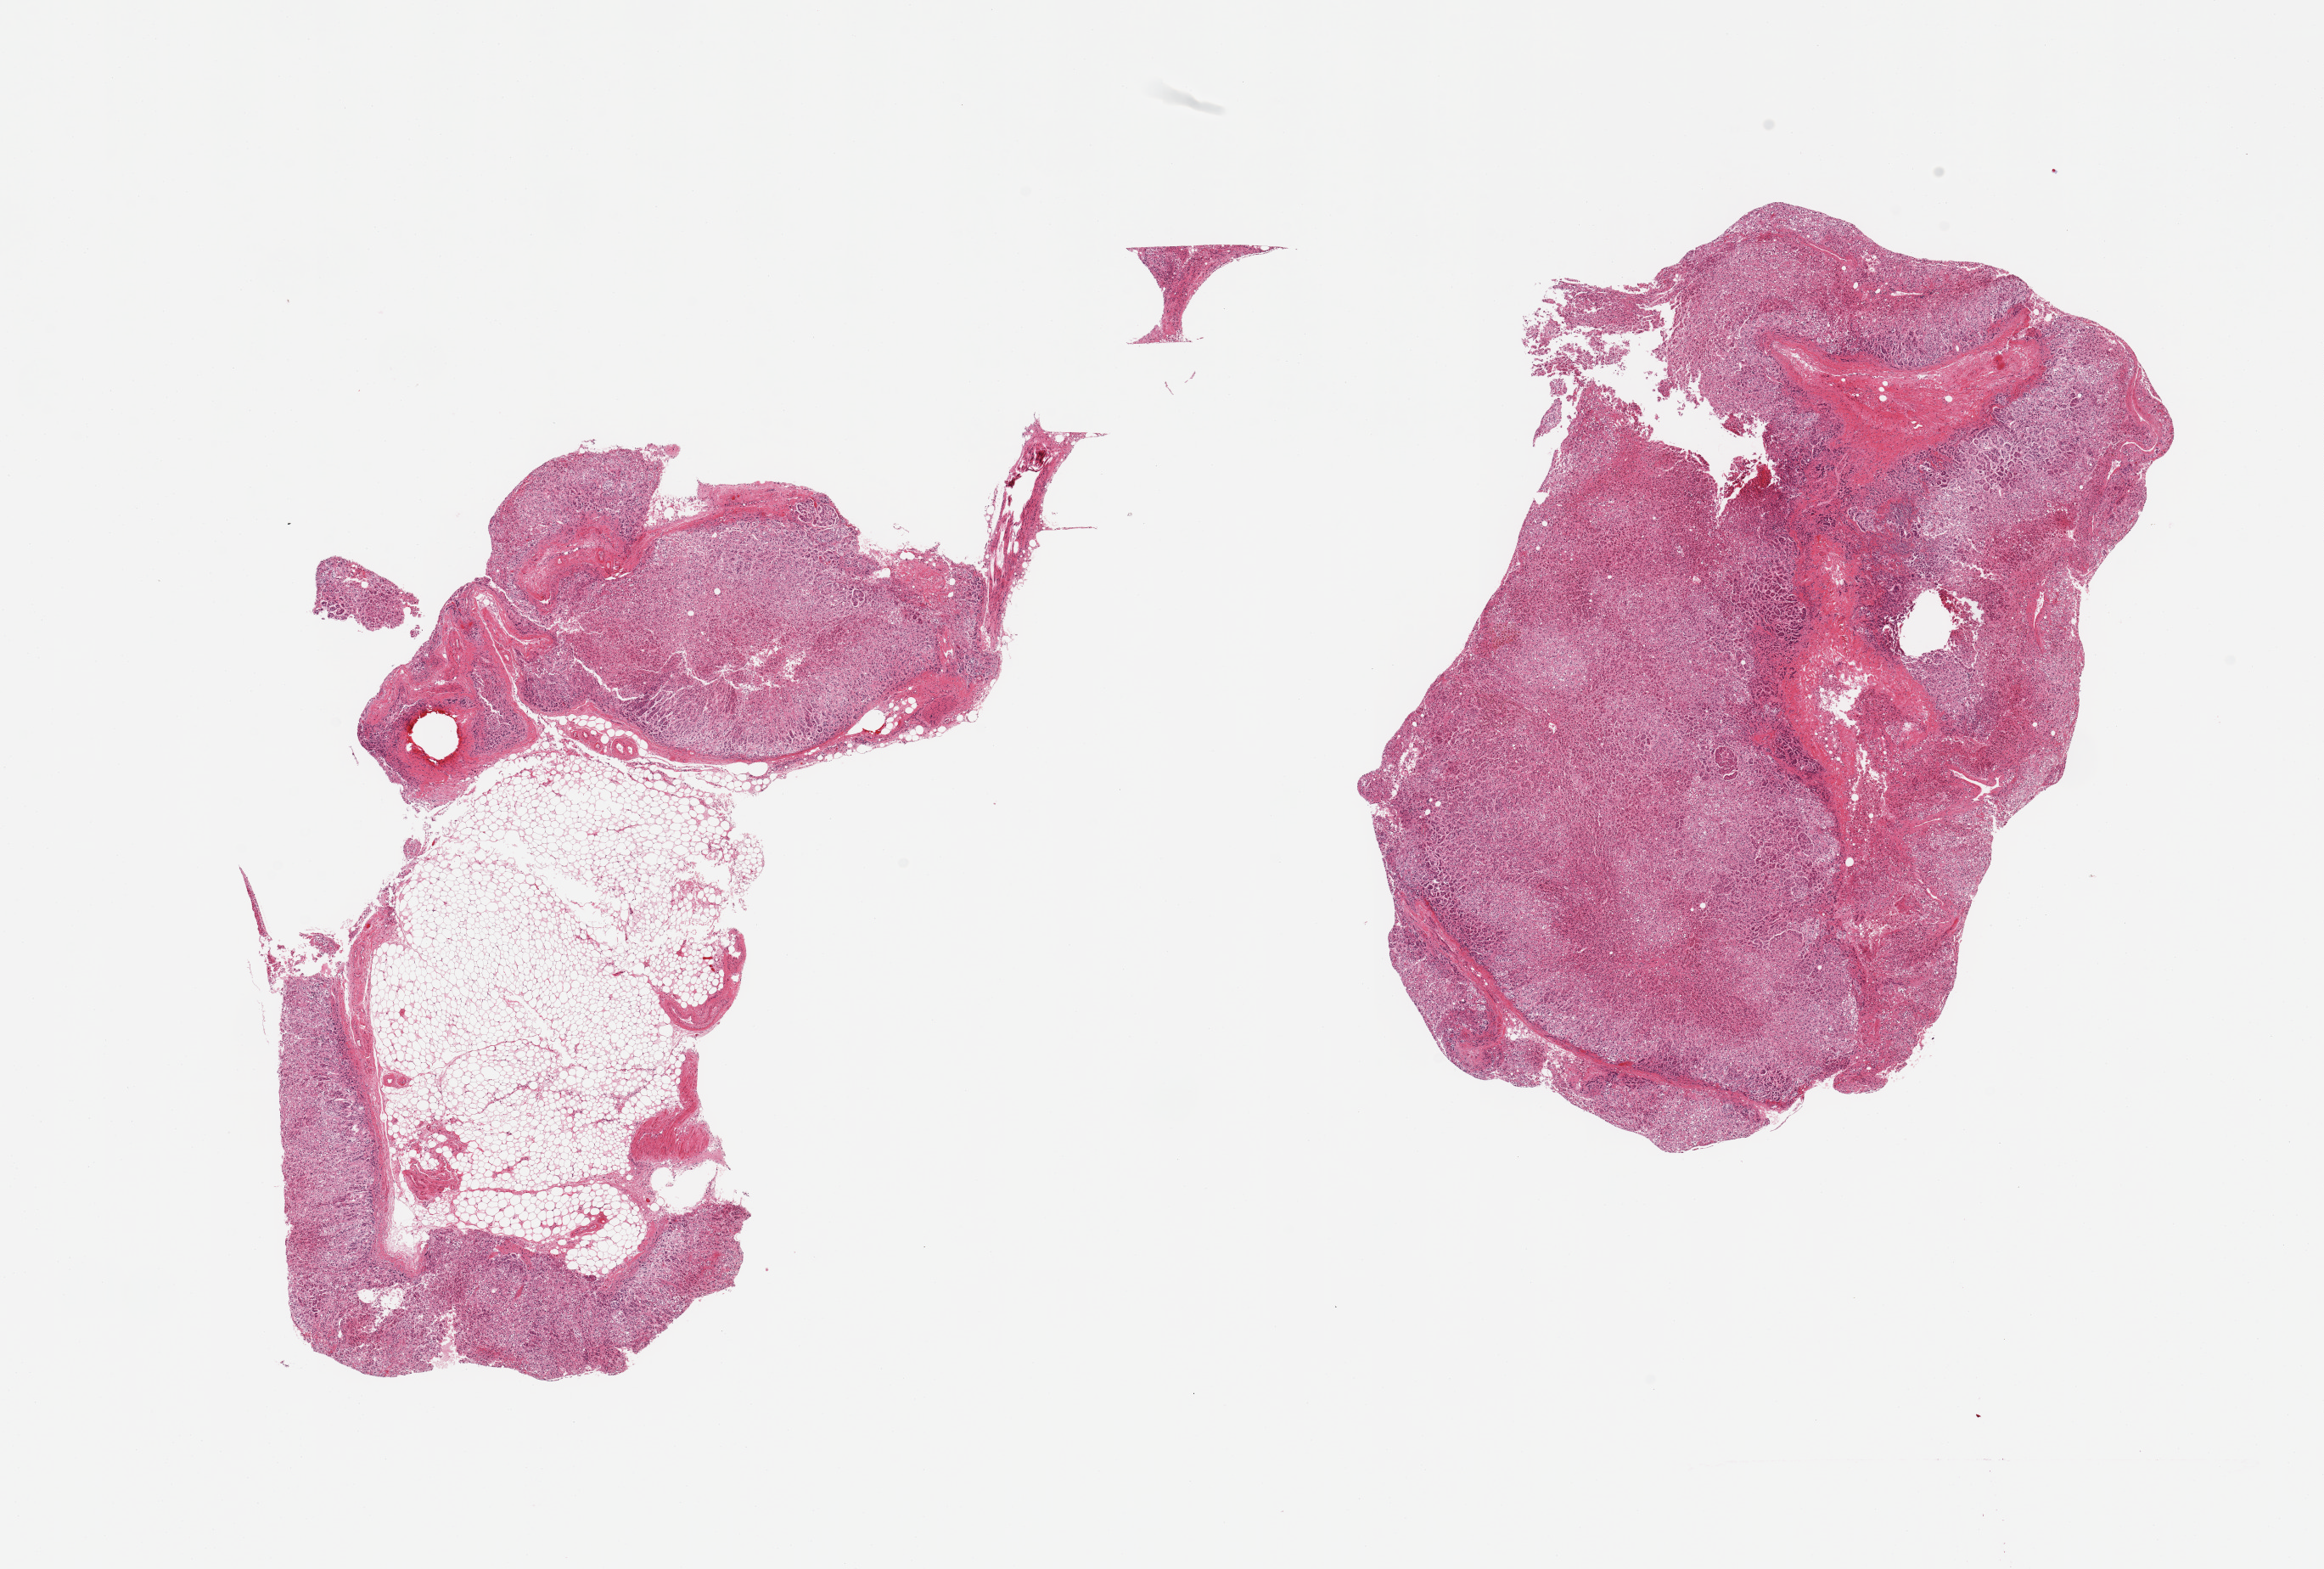
Whole-slide image, haematoxylin and eosin stain — a low-resolution overview of the entire scanned area, about 21.7 x 14.6 mm (from a 20x scan). PAXgene-fixed, paraffin-embedded tissue. Section of adrenal gland (target tissue). Tissue donor sample. Donor: female.
Pathologist's review note for this sample: 2 pieces: 1 with 50% external fat.